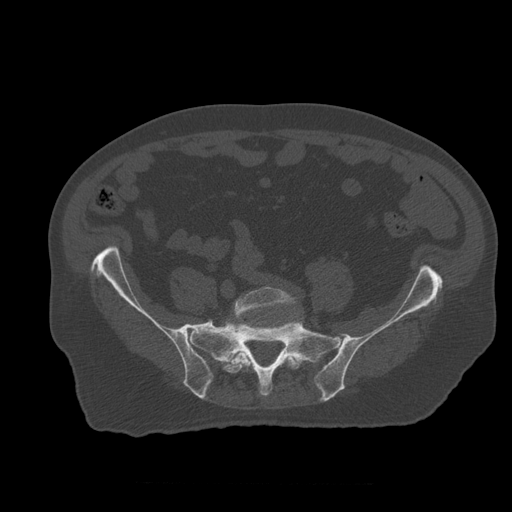
CT including the spine, one axial slice; position 128 of 399 along the scan axis; bone window (W 1800 / L 400 HU); 1.25 mm slice thickness; 512 × 512 image matrix. Patient age 73 years. Case-level facts recorded for this patient, not image findings: primary cancer: prostate.
Annotated regions visible in this slice (semi-automatically segmented with operator editing):
- L5 vertebra: bounding box (x1, y1, x2, y2) in pixels: (223, 287, 301, 374)